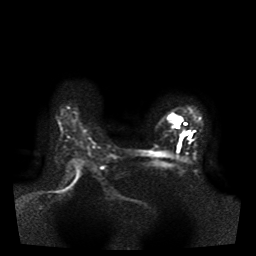
Breast MRI, one axial slice; slice 31 of 41 in the series (ordered by position); diffusion-weighted series; image 2 of 4 stored at this slice position (different b-values; order by instance number); 1.5 T; 5 mm slice thickness; 256 × 256 image matrix, field of view 330 × 330 mm. Female patient.
Outlined on this slice (expert manual segmentation):
- tumour on diffusion-weighted imaging: bounding box <167,115,179,124> (left, top, right, bottom; pixels)